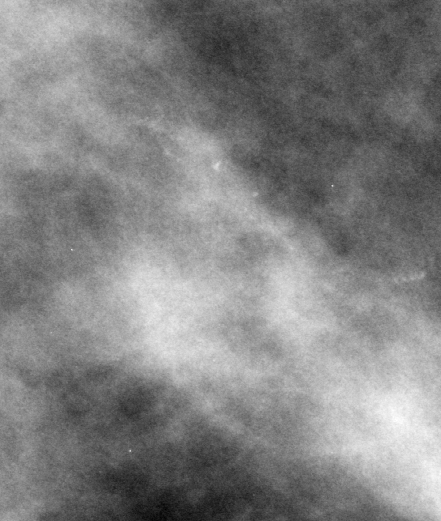
Cropped region of a digitized screen-film mammogram centred on a radiologist-marked abnormality; left breast; CC view.
- Calcifications, morphology amorphous, distribution clustered; BI-RADS assessment category 4; pathology result (as recorded, not read from the image): malignant.